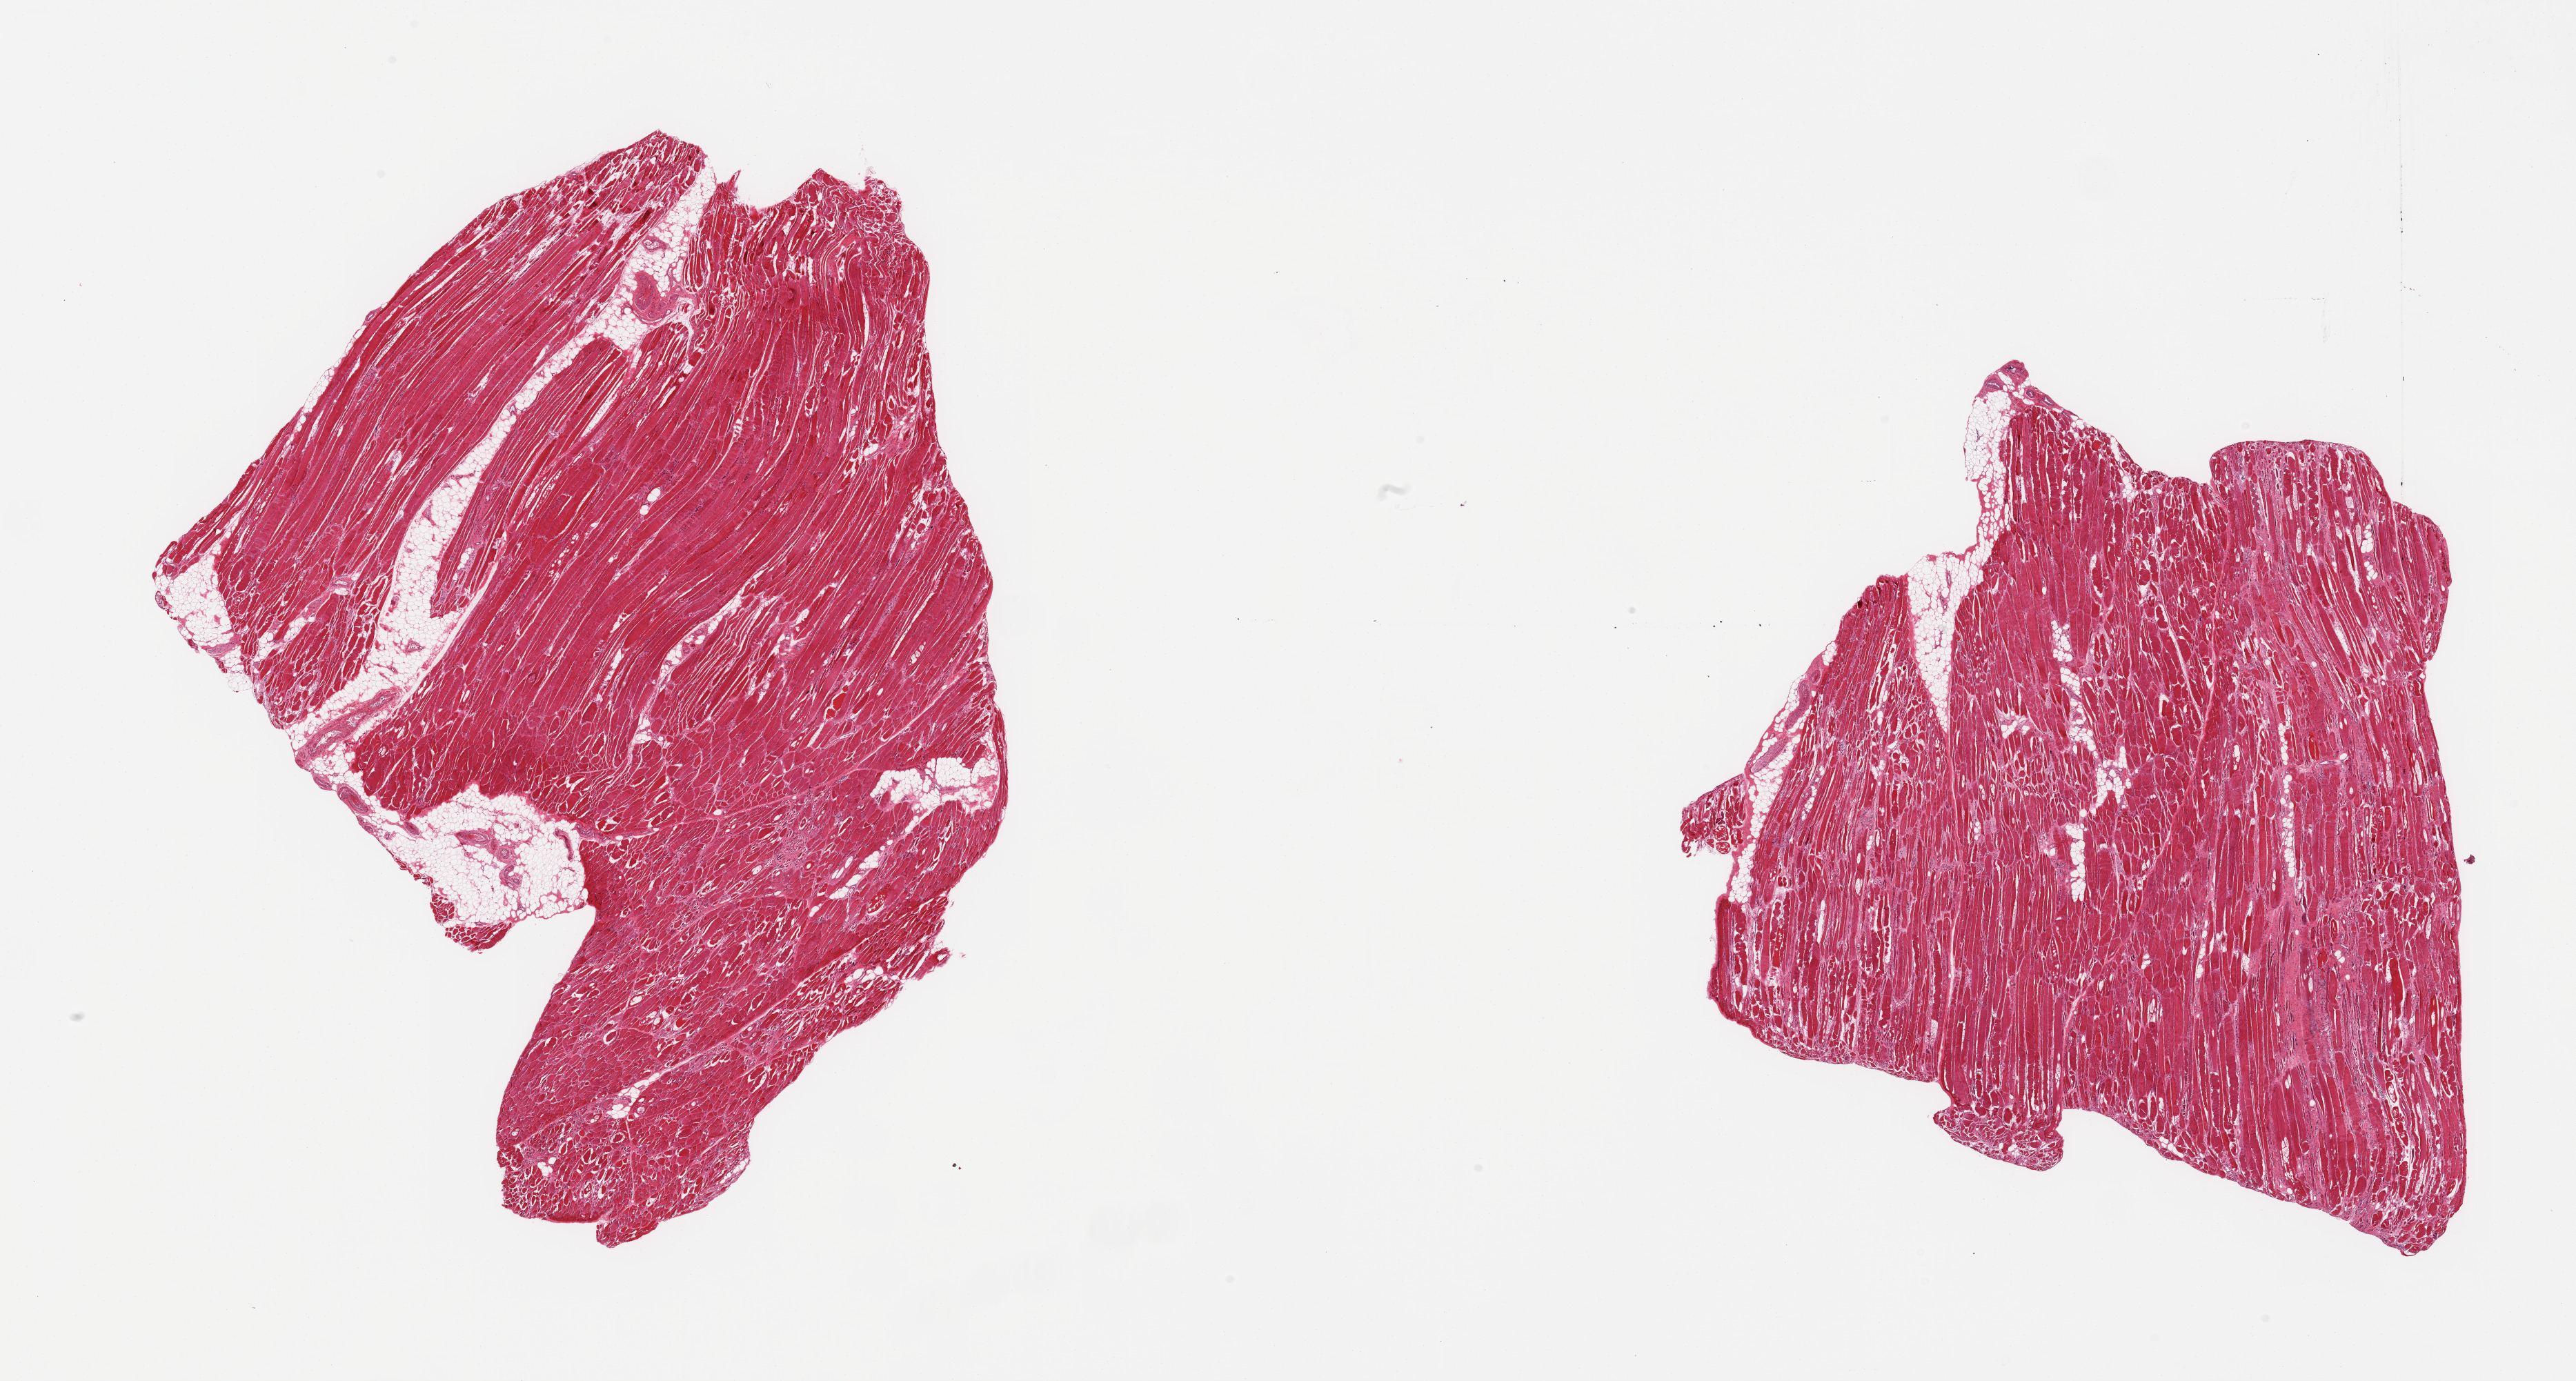
Digitized haematoxylin and eosin-stained section, brightfield — shown as a low-resolution overview of the whole scanned area (about 29.5 x 15.8 mm, slide scanned at 20x); PAXgene-fixed, paraffin-embedded tissue; target tissue: skeletal muscle; tissue donor sample. Donor: male.
* pathologist's review note for this sample: 2 pieces, ~10% interstitial fat/vascular elements; foci of scarring/resolved myositis